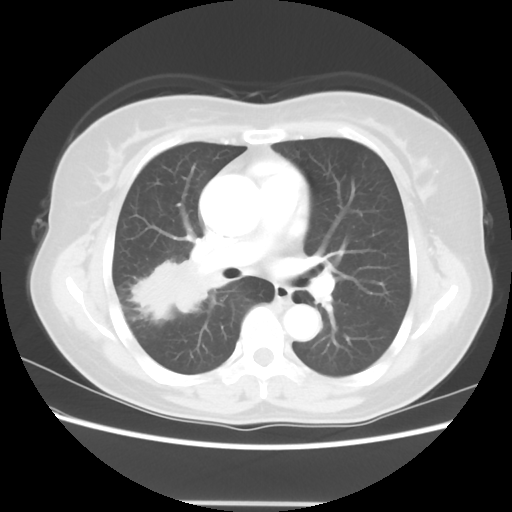
Chest CT, one axial slice. Position 34 of 56 along the scan axis. Lung window (W 1500 / L -600 HU). 5 mm slice thickness. 512 × 512 image matrix. Patient: female, 55 years. Case-level facts recorded for this patient, not image findings: clinical TNM (as recorded): T2 N1 M0.
Outlined on this slice (rectangle marked by the reading radiologist):
- lung tumour (recorded histology: adenocarcinoma): box from (x=123, y=239) to (x=217, y=321) px